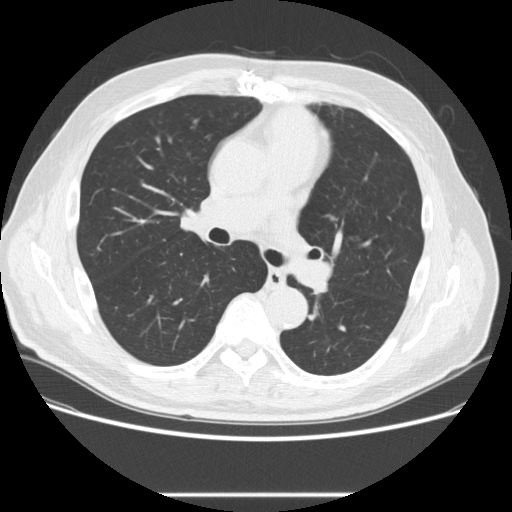
Low-dose screening chest CT, axial slice; second screening round (one year after baseline); lung window (W 1500 / L -600 HU); standard (soft-tissue) reconstruction kernel (STANDARD); slice 97 of 268 in the series. Male participant, aged 66 years at enrolment.
• Lesion marked by an expert reader, bounding box (x1, y1, x2, y2) in pixels: (320, 203, 351, 234).
• Screening reader's record for this exam (one nodule recorded; not confirmed to be the boxed lesion): non-calcified nodule or mass ≥4 mm, right lower lobe, 4 × 4 mm, smooth margins, soft tissue attenuation, pre-existing on the prior screen: yes; interval growth: no.
• Note: the box lies in the patient's left hemithorax on this image, whereas the reader's record names the right lung; they may be different findings.
• Participant outcome: lung cancer diagnosed 449 days after this screen (after the third annual screen) — squamous cell carcinoma, NOS, left upper lobe, poorly differentiated (G3), stage IA (AJCC 6th edition), 27 mm at pathology.